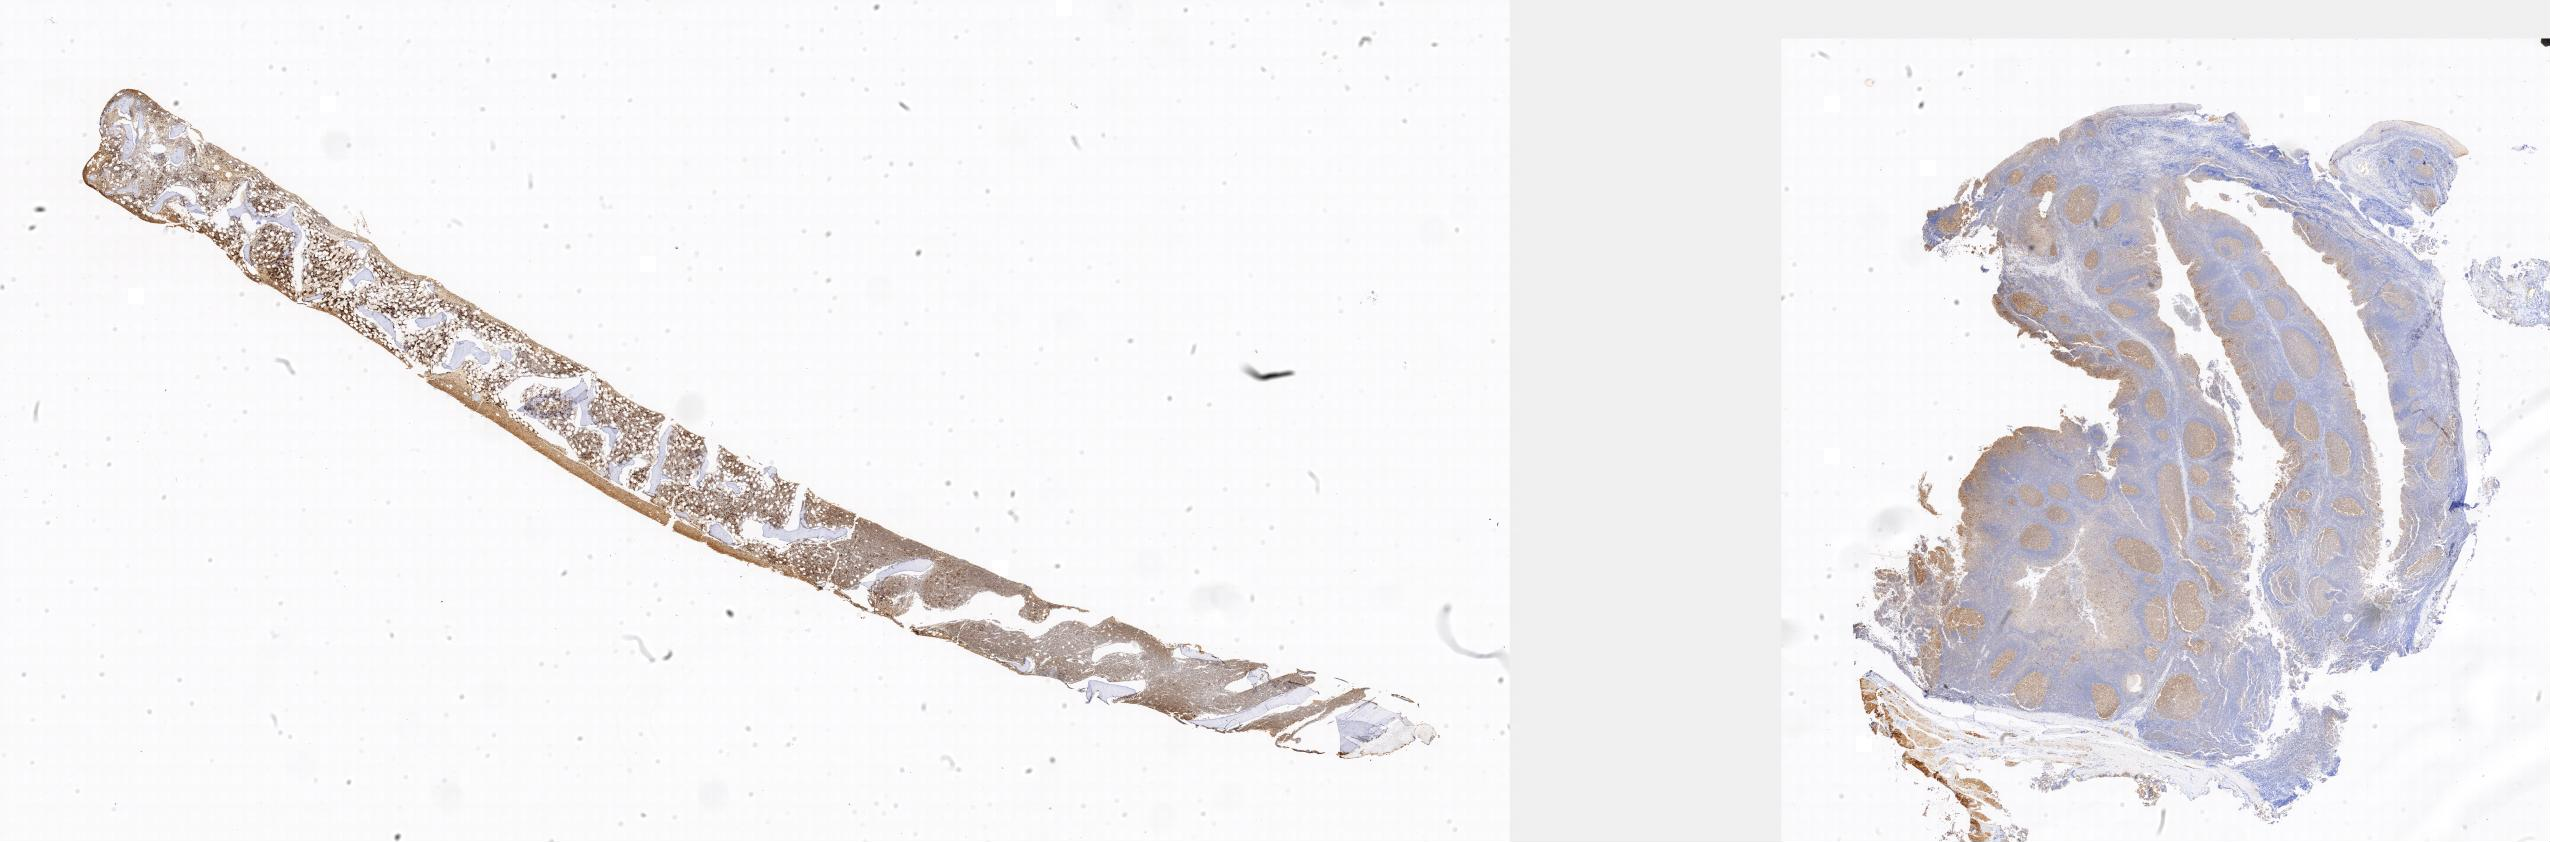
Whole-slide image, immunohistochemical stain for BCL6, whole scanned area shown as a low-resolution overview, tumor tissue. Patient male; 12 years old.
Diagnosis: Burkitt lymphoma, NOS.